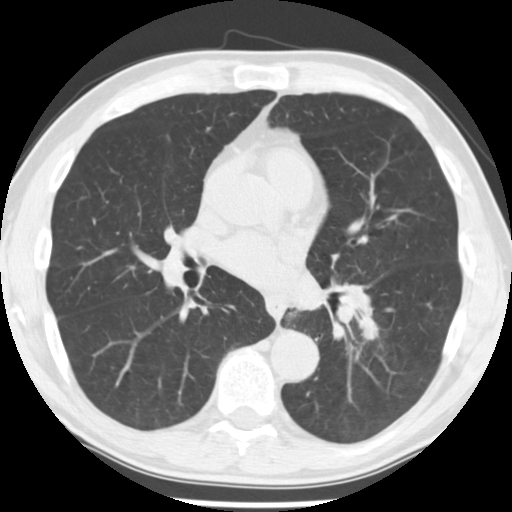
Axial slice from a low-dose chest CT screening exam, third annual screen, lung window (W 1500 / L -600 HU). Male, age 64 years at enrolment. Current smoker at enrolment.
• Lesion marked by an expert reader, box from (x=350, y=316) to (x=390, y=352) px.
• No non-calcified nodule or mass ≥4 mm was recorded by the screening reader at this exam.
• Participant outcome: lung cancer diagnosed 203 days after this screen — adenocarcinoma, NOS, left lower lobe, stage IV (AJCC 6th edition), 44 mm at pathology.